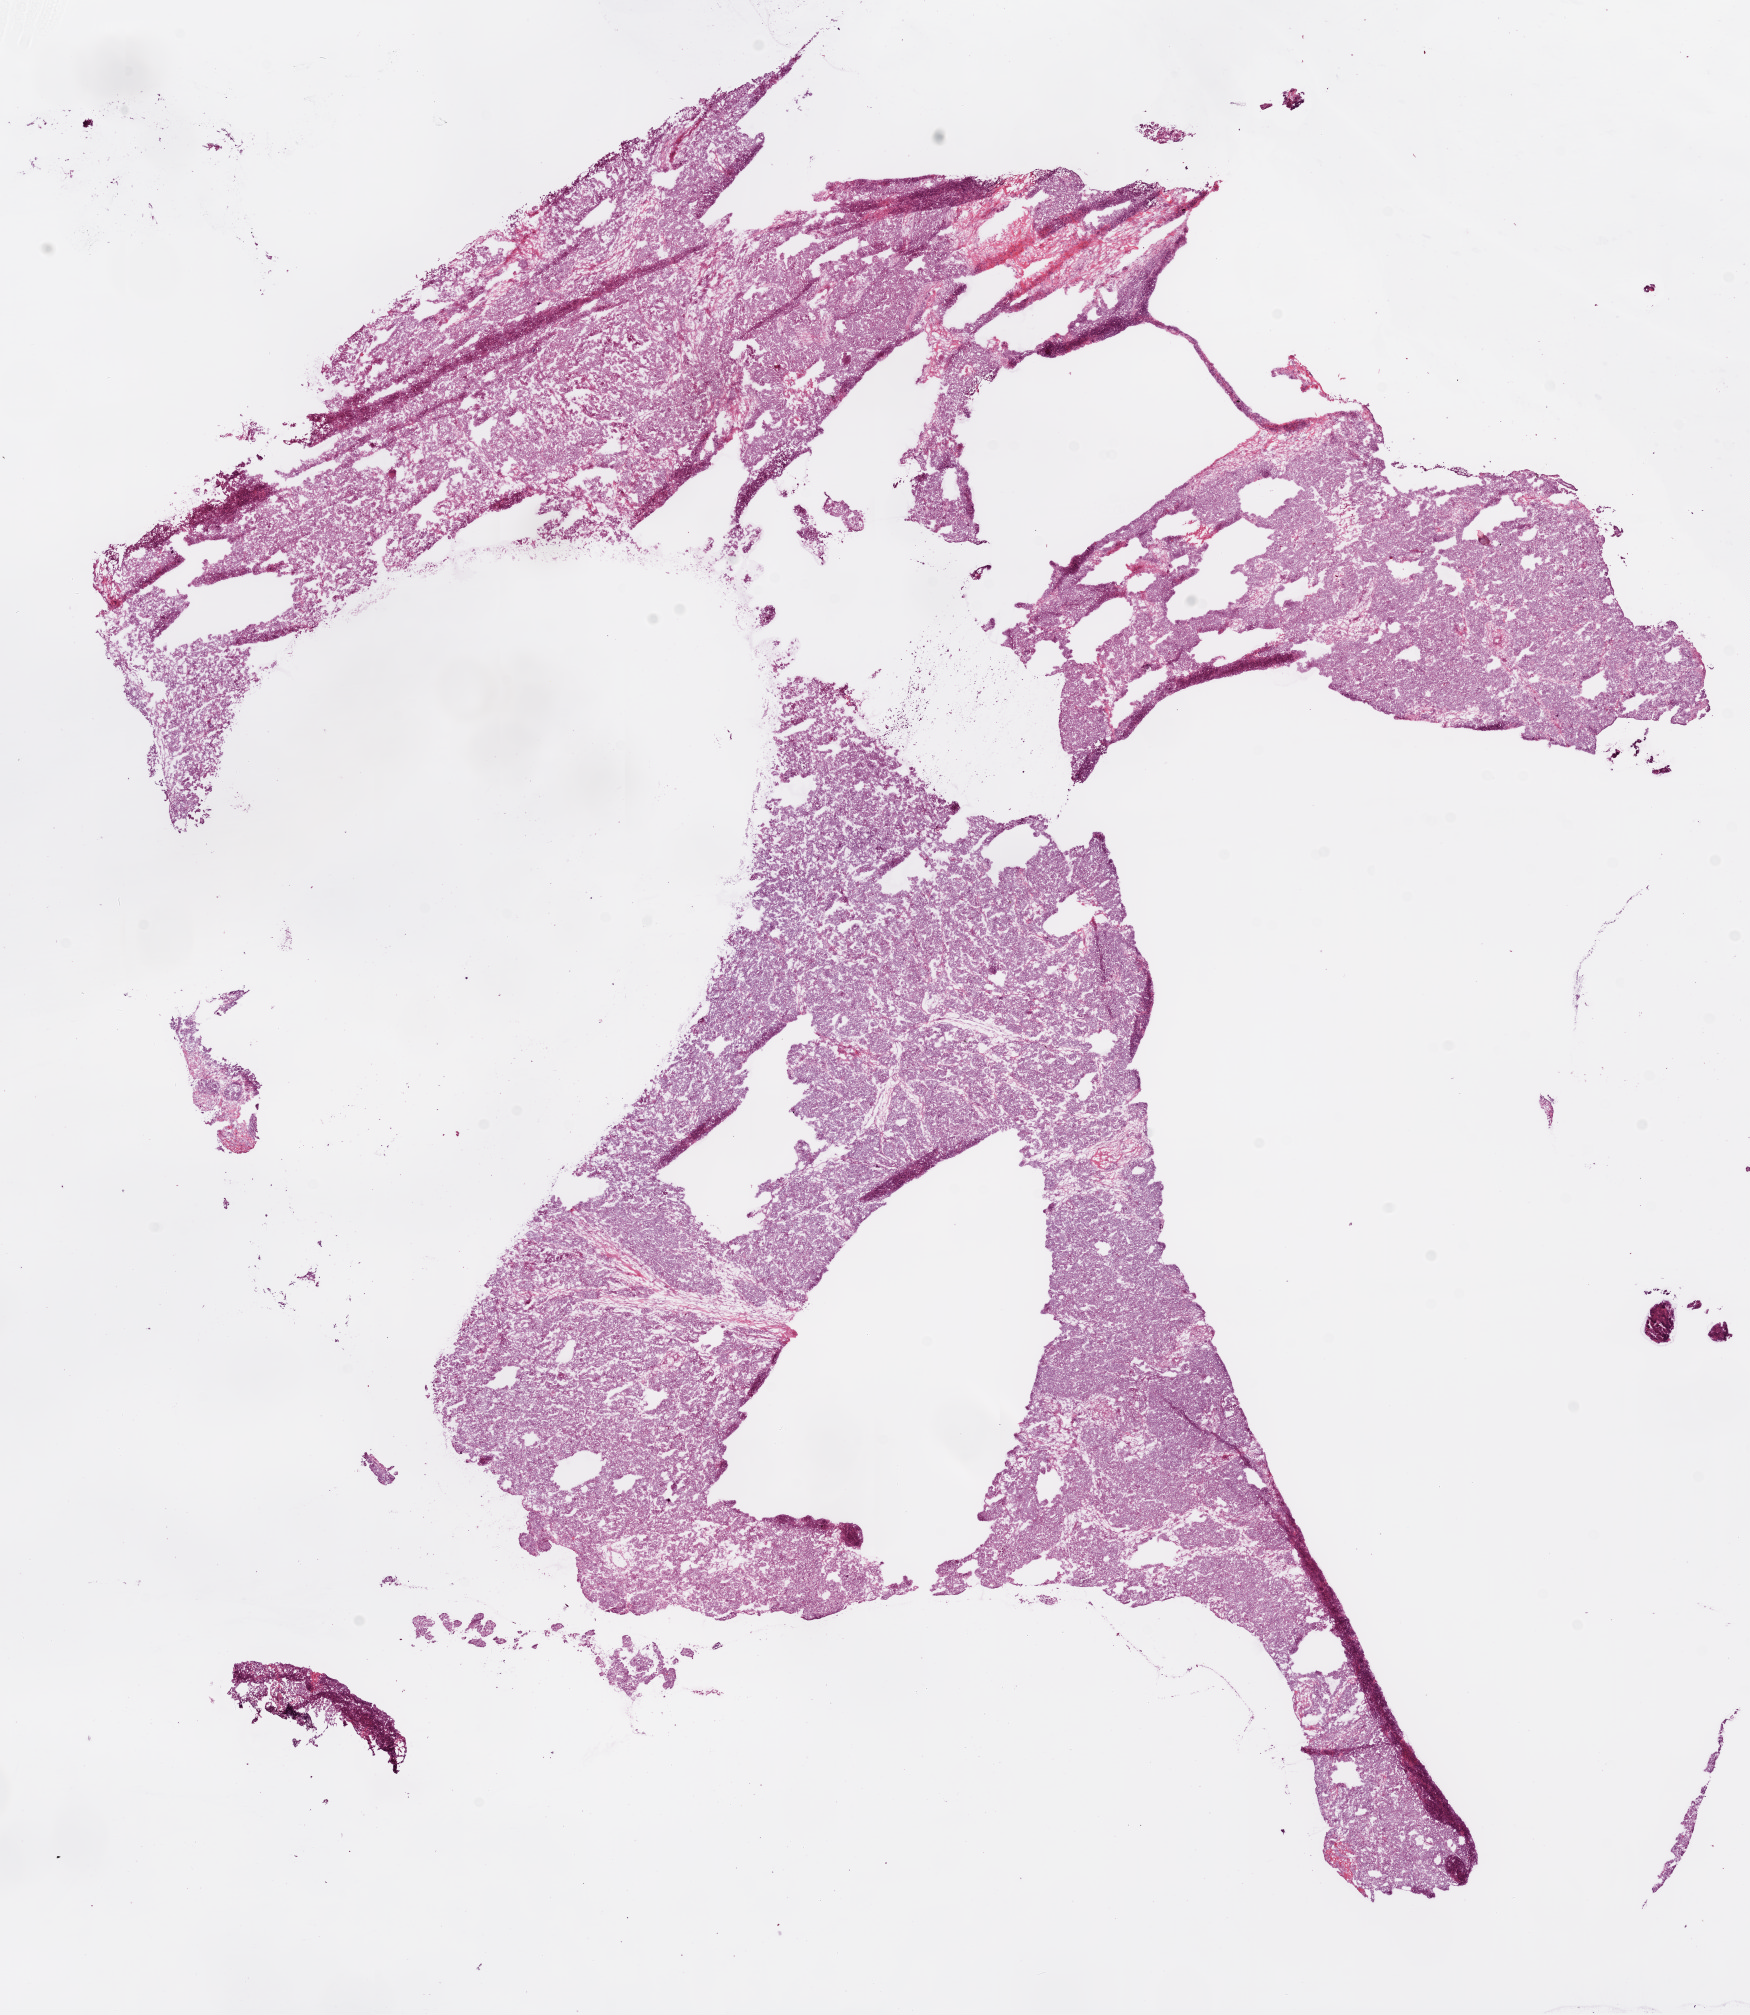
Hematoxylin and eosin (H&E) stained whole-slide image, low-resolution overview of the scanned area, about 14.0 x 16.2 mm. Frozen section. Recurrent tumour sample from the ovary. Patient: female, age at initial diagnosis 53 years. Slide review estimates, as recorded: tumour cells 95%, tumour nuclei 90%, normal cells 0%, stromal cells 5%, necrosis 0%. Infiltration values recorded for this section: neutrophil infiltration 0%.
This section: recurrent tumour. Patient diagnosis: Serous surface papillary carcinoma.